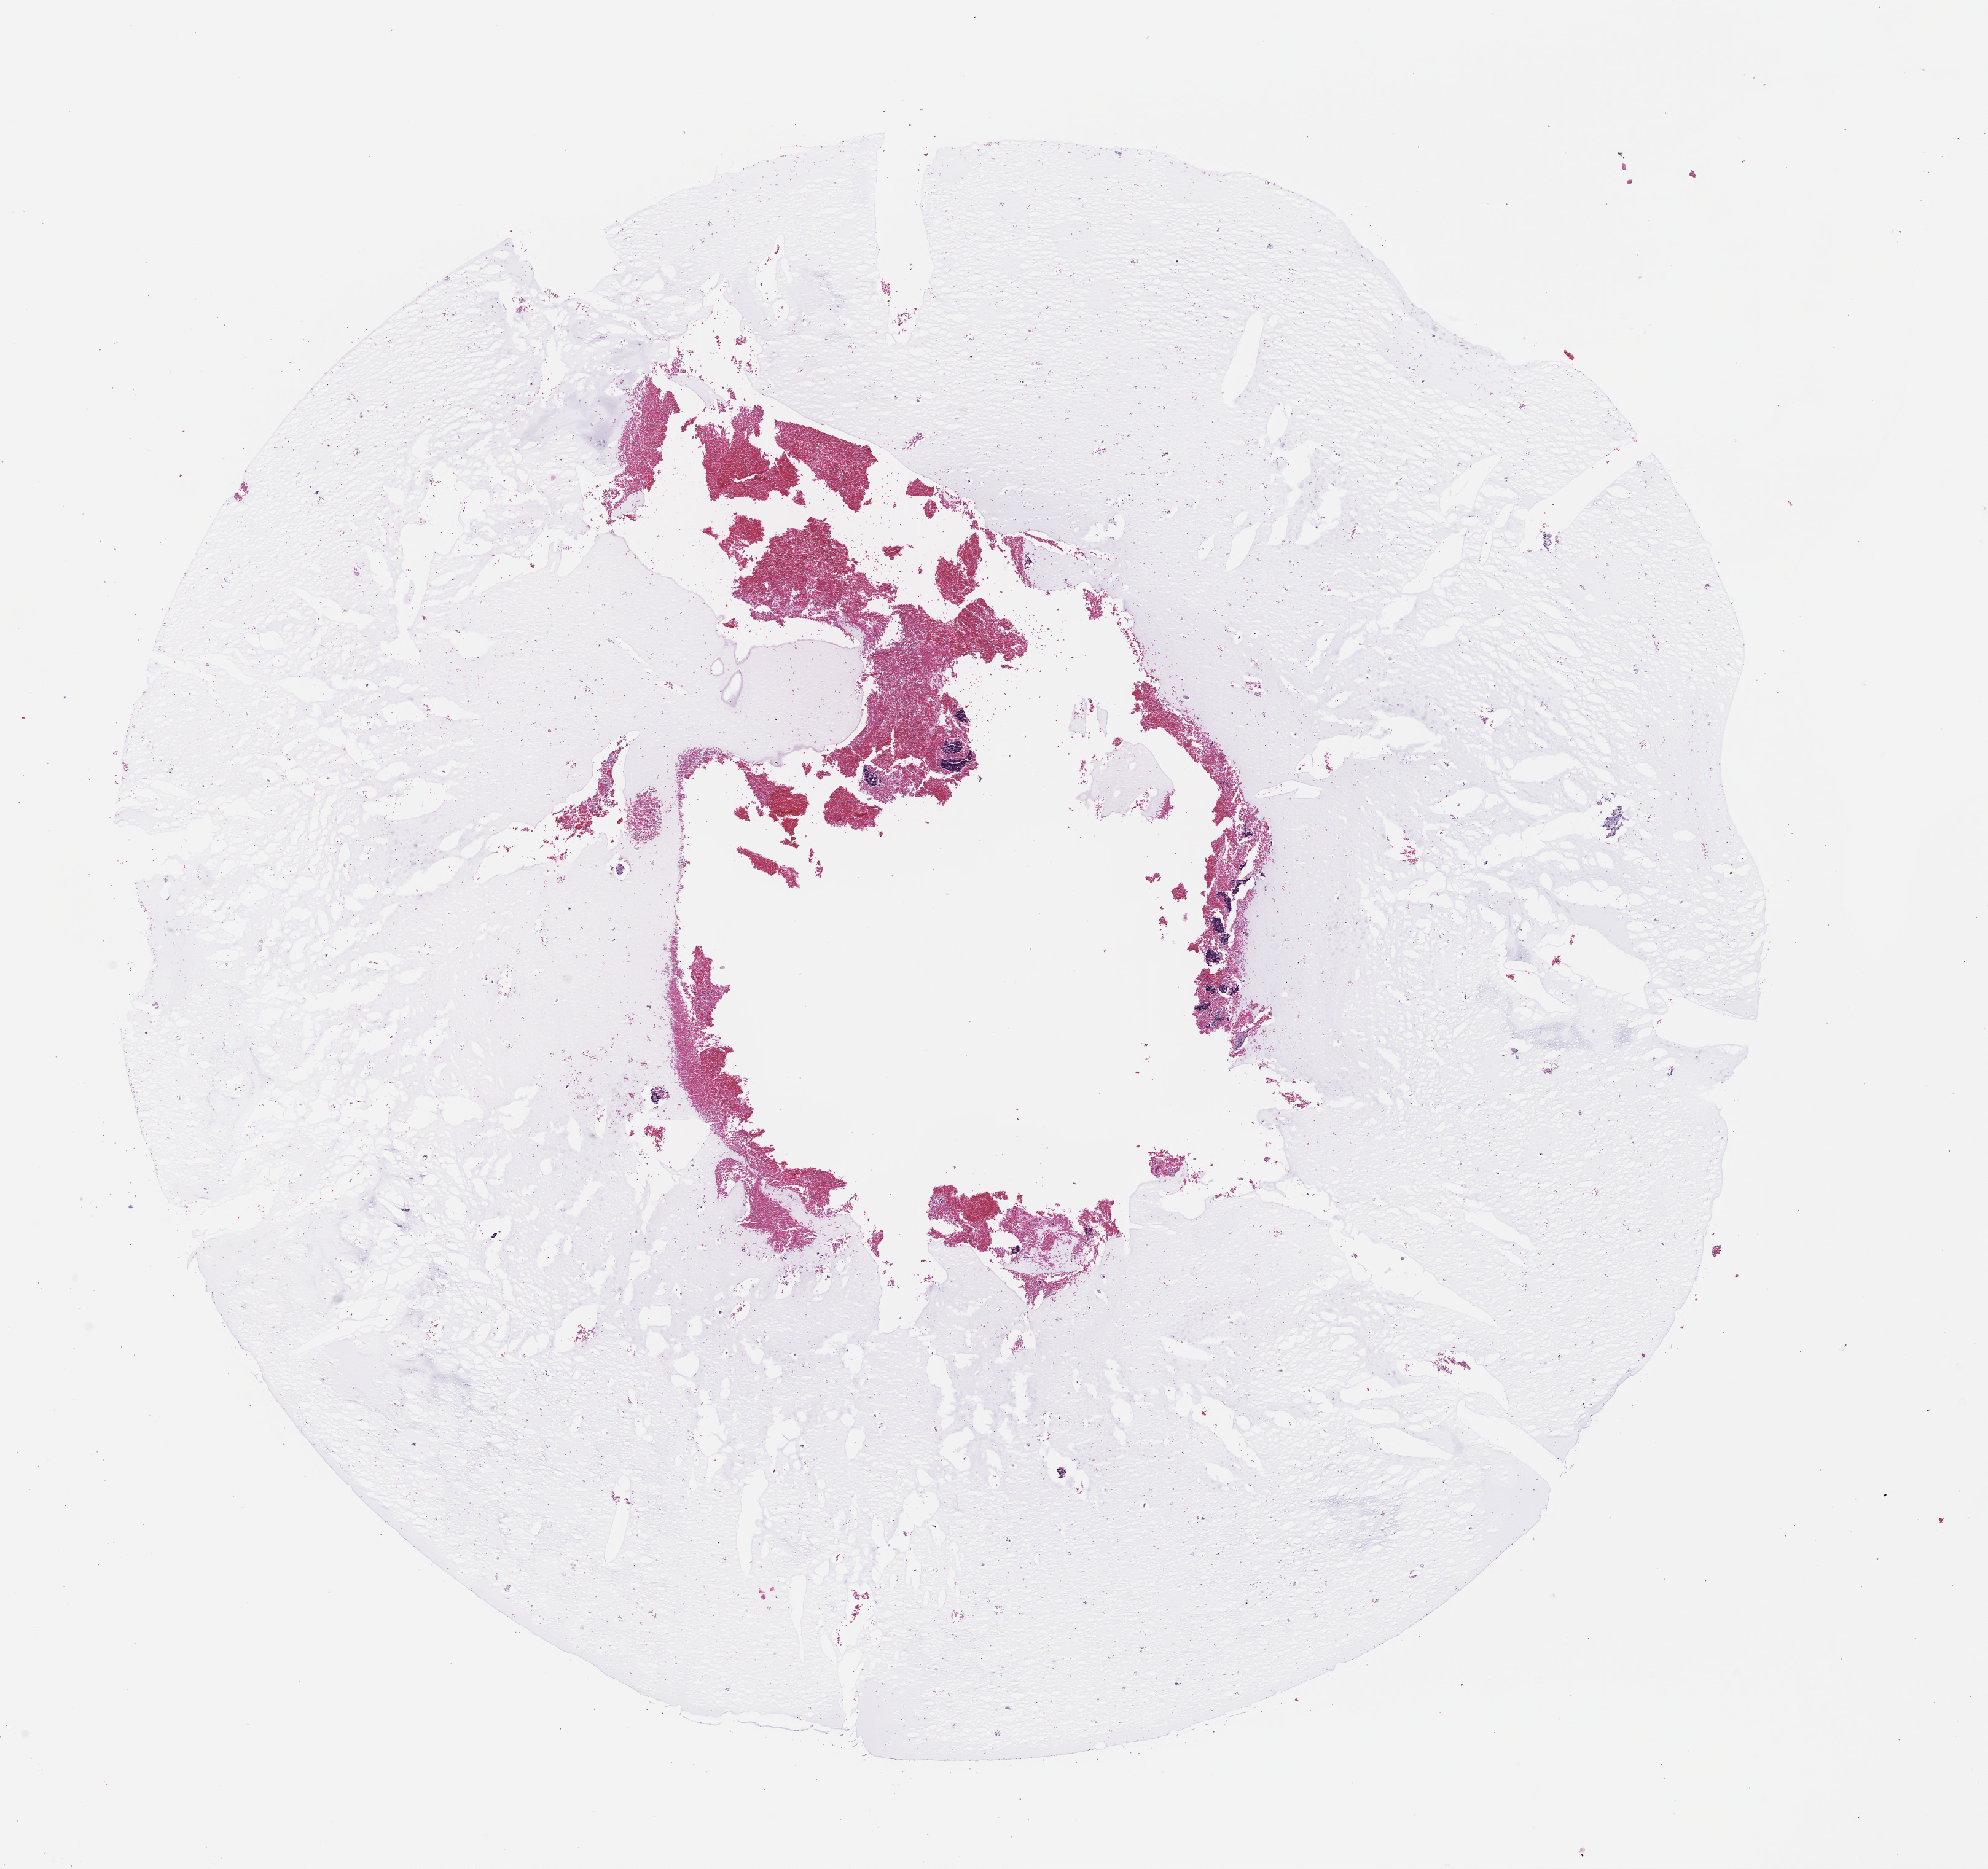
Hematoxylin and eosin (H&E) whole-slide image — shown as a low-resolution overview of the whole scanned area (about 13.1 x 12.3 mm); formalin-fixed, paraffin-embedded (FFPE) tissue; specimen time point: archival tissue. Male patient.
* this section: metastasis (sampled organ not recorded)
* patient diagnosis (primary): Prostate Carcinoma